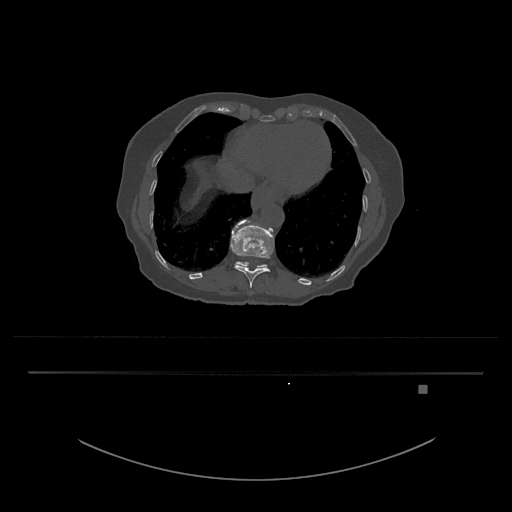
CT including the spine, one axial slice. Slice 653 of 797 in the series (ordered by position). Bone window (W 1800 / L 400 HU). 0.5 mm slice thickness. 512 × 512 image matrix, field of view 500 × 500 mm. Patient: female, 57 years. From the clinical record (not read from this slice): primary cancer: cervical.
Structures marked on this image (semi-automatic segmentation, software-assisted and operator-edited):
- T11 vertebra: bounding box <230,219,274,289> (left, top, right, bottom; pixels)
- T12 vertebra: <235,261,268,269>